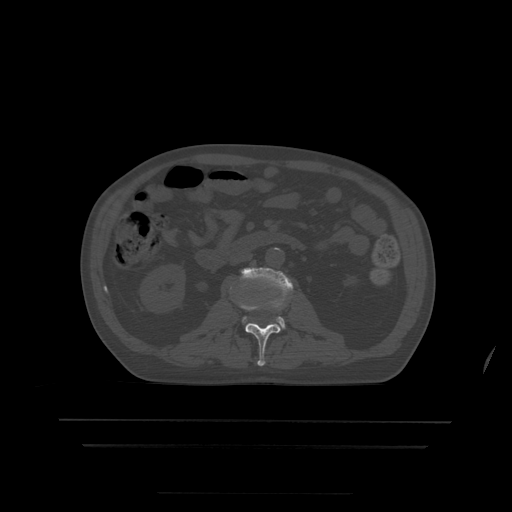
CT including the spine, one axial slice; position 136 of 522 along the scan axis; bone window (W 1800 / L 400 HU); 1.25 mm slice thickness; 512 × 512 image matrix, field of view 436 × 436 mm. Patient age 68 years. Case-level facts recorded for this patient, not image findings: primary cancer: urothelial.
Annotated regions visible in this slice (semi-automatic segmentation, software-assisted and operator-edited):
- L2 vertebra: bounding box (x1, y1, x2, y2) in pixels: (238, 303, 280, 367)
- L3 vertebra: (242, 268, 294, 328)